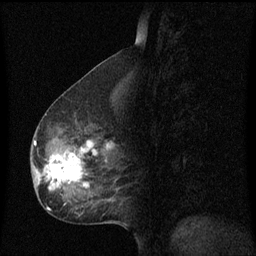
Breast MRI (dynamic contrast-enhanced), one sagittal slice; dynamic contrast-enhanced series, image 2 of 3 at this slice position (ordered by acquisition); 1.5 T; TE 4.2 ms, TR 8.4 ms; 2 mm slice thickness; 256 × 256 image matrix. Patient: female, 49 years. From the clinical record (not read from this slice): setting: breast cancer imaged before/during neoadjuvant chemotherapy; receptor status: HR-positive, HER2-negative.
Annotated regions visible in this slice (semi-automatically segmented with operator editing):
- analysis volume of interest (the breast-tissue region the enhancement analysis was run in; not a lesion): bounding box [x1, y1, x2, y2] px = [31, 126, 120, 201]
- tumour enhancement mask (voxels above the 70 % enhancement threshold inside the analysis volume of interest): [35, 142, 112, 191]